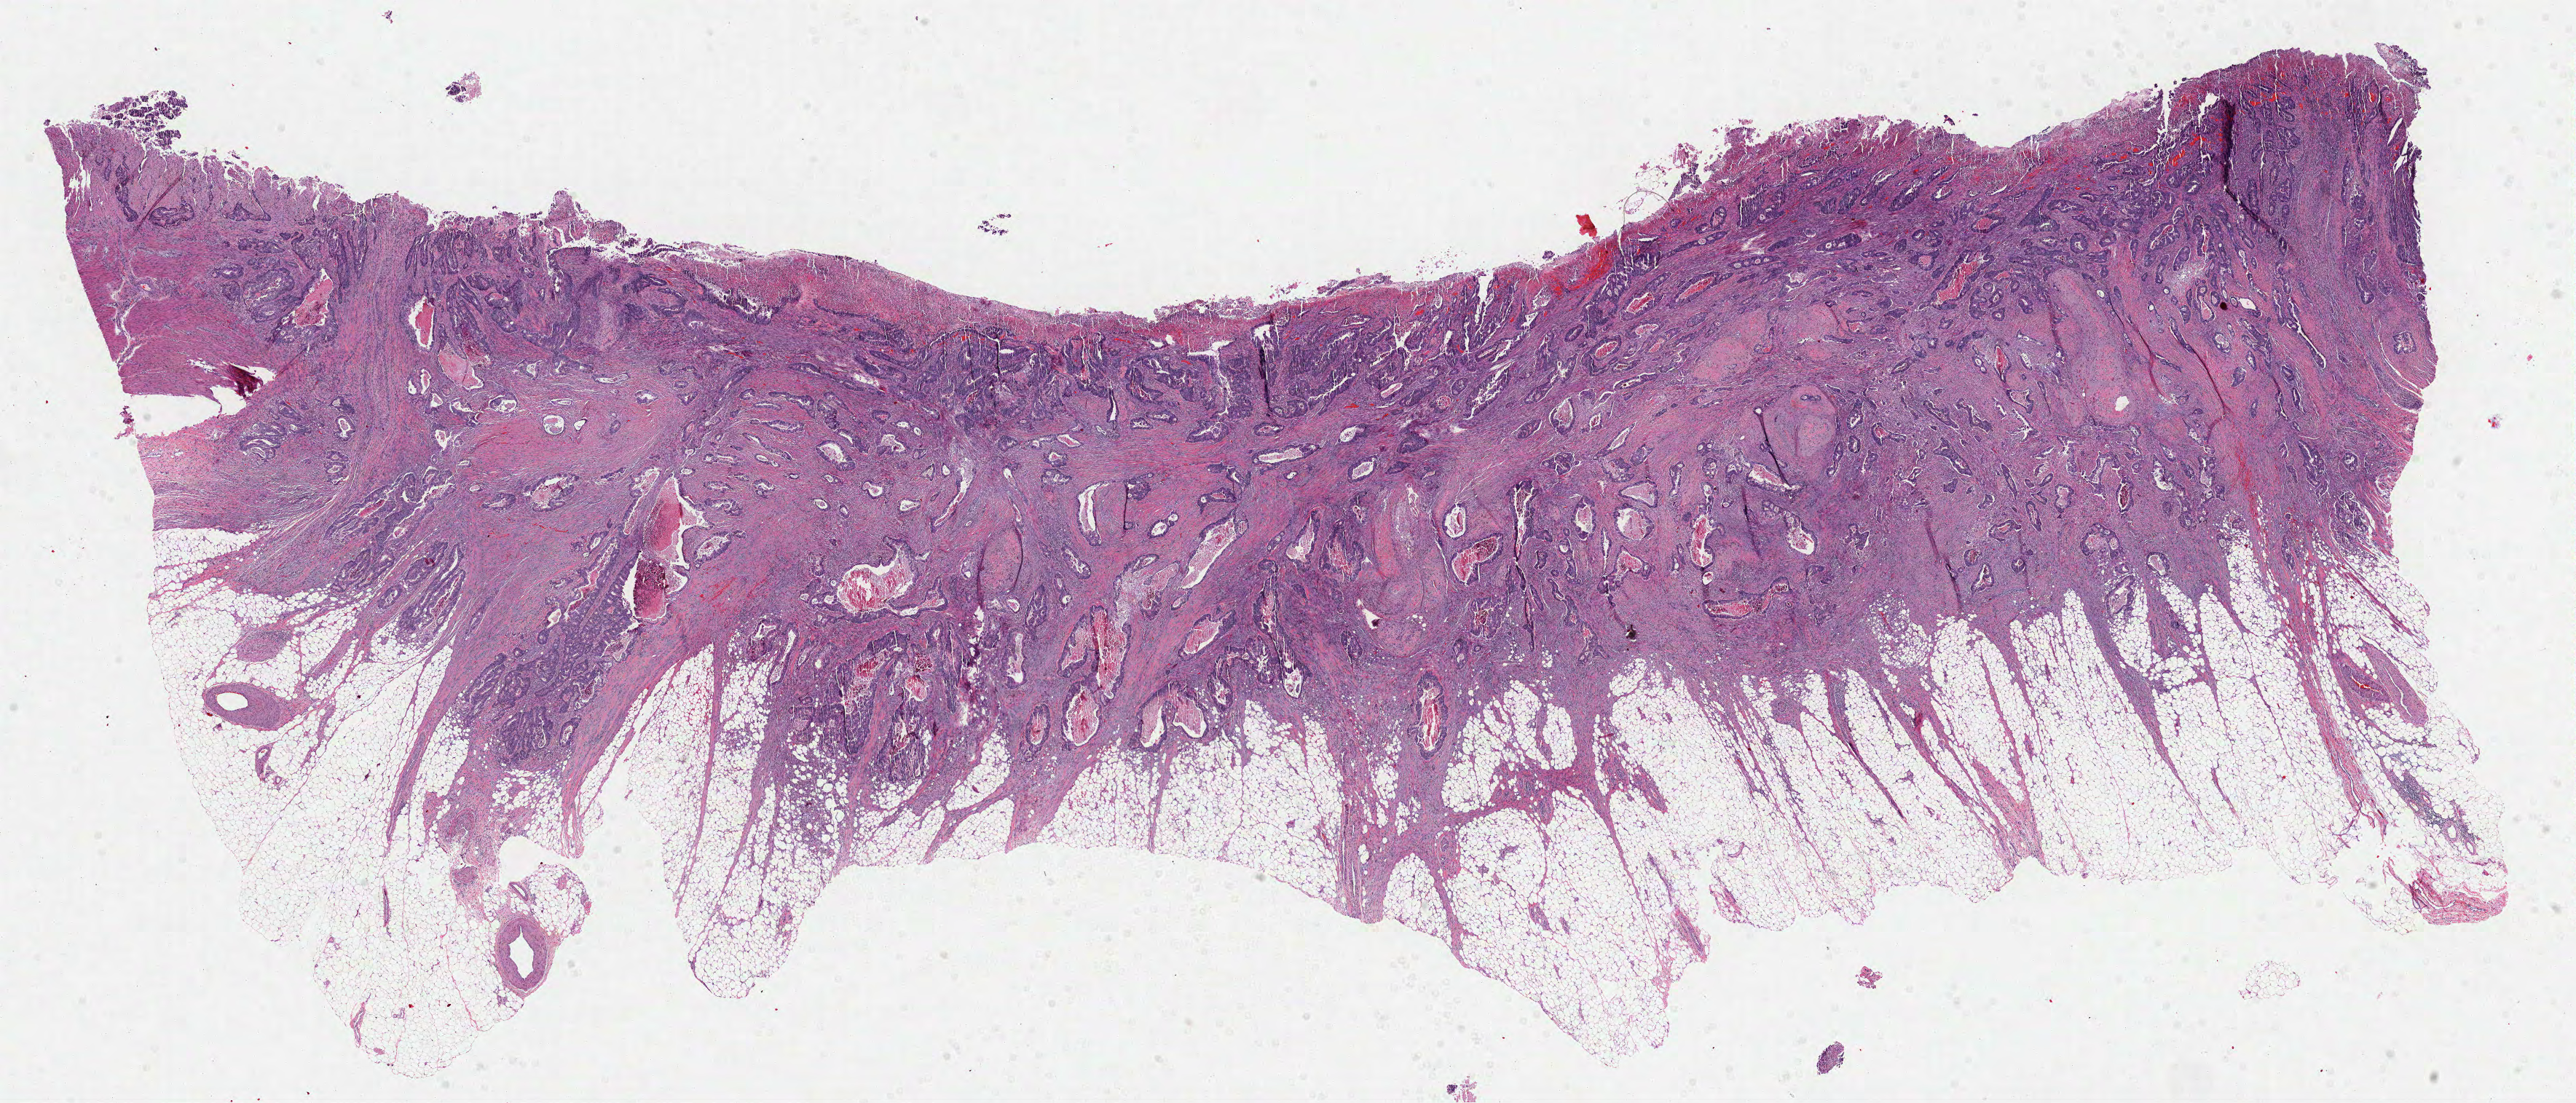
Digitized Hematoxylin and eosin (H&E) stained tissue section (whole slide), whole scanned area (about 28.5 x 12.2 mm) shown as a low-resolution overview; FFPE section; sample: primary tumour, rectum. Female, age 57 years at initial diagnosis.
• AJCC pathologic stage: IVA
• histologic diagnosis: Adenocarcinoma, NOS (rectosigmoid junction)
• lymph nodes positive (case pathology): 8 of 39 examined